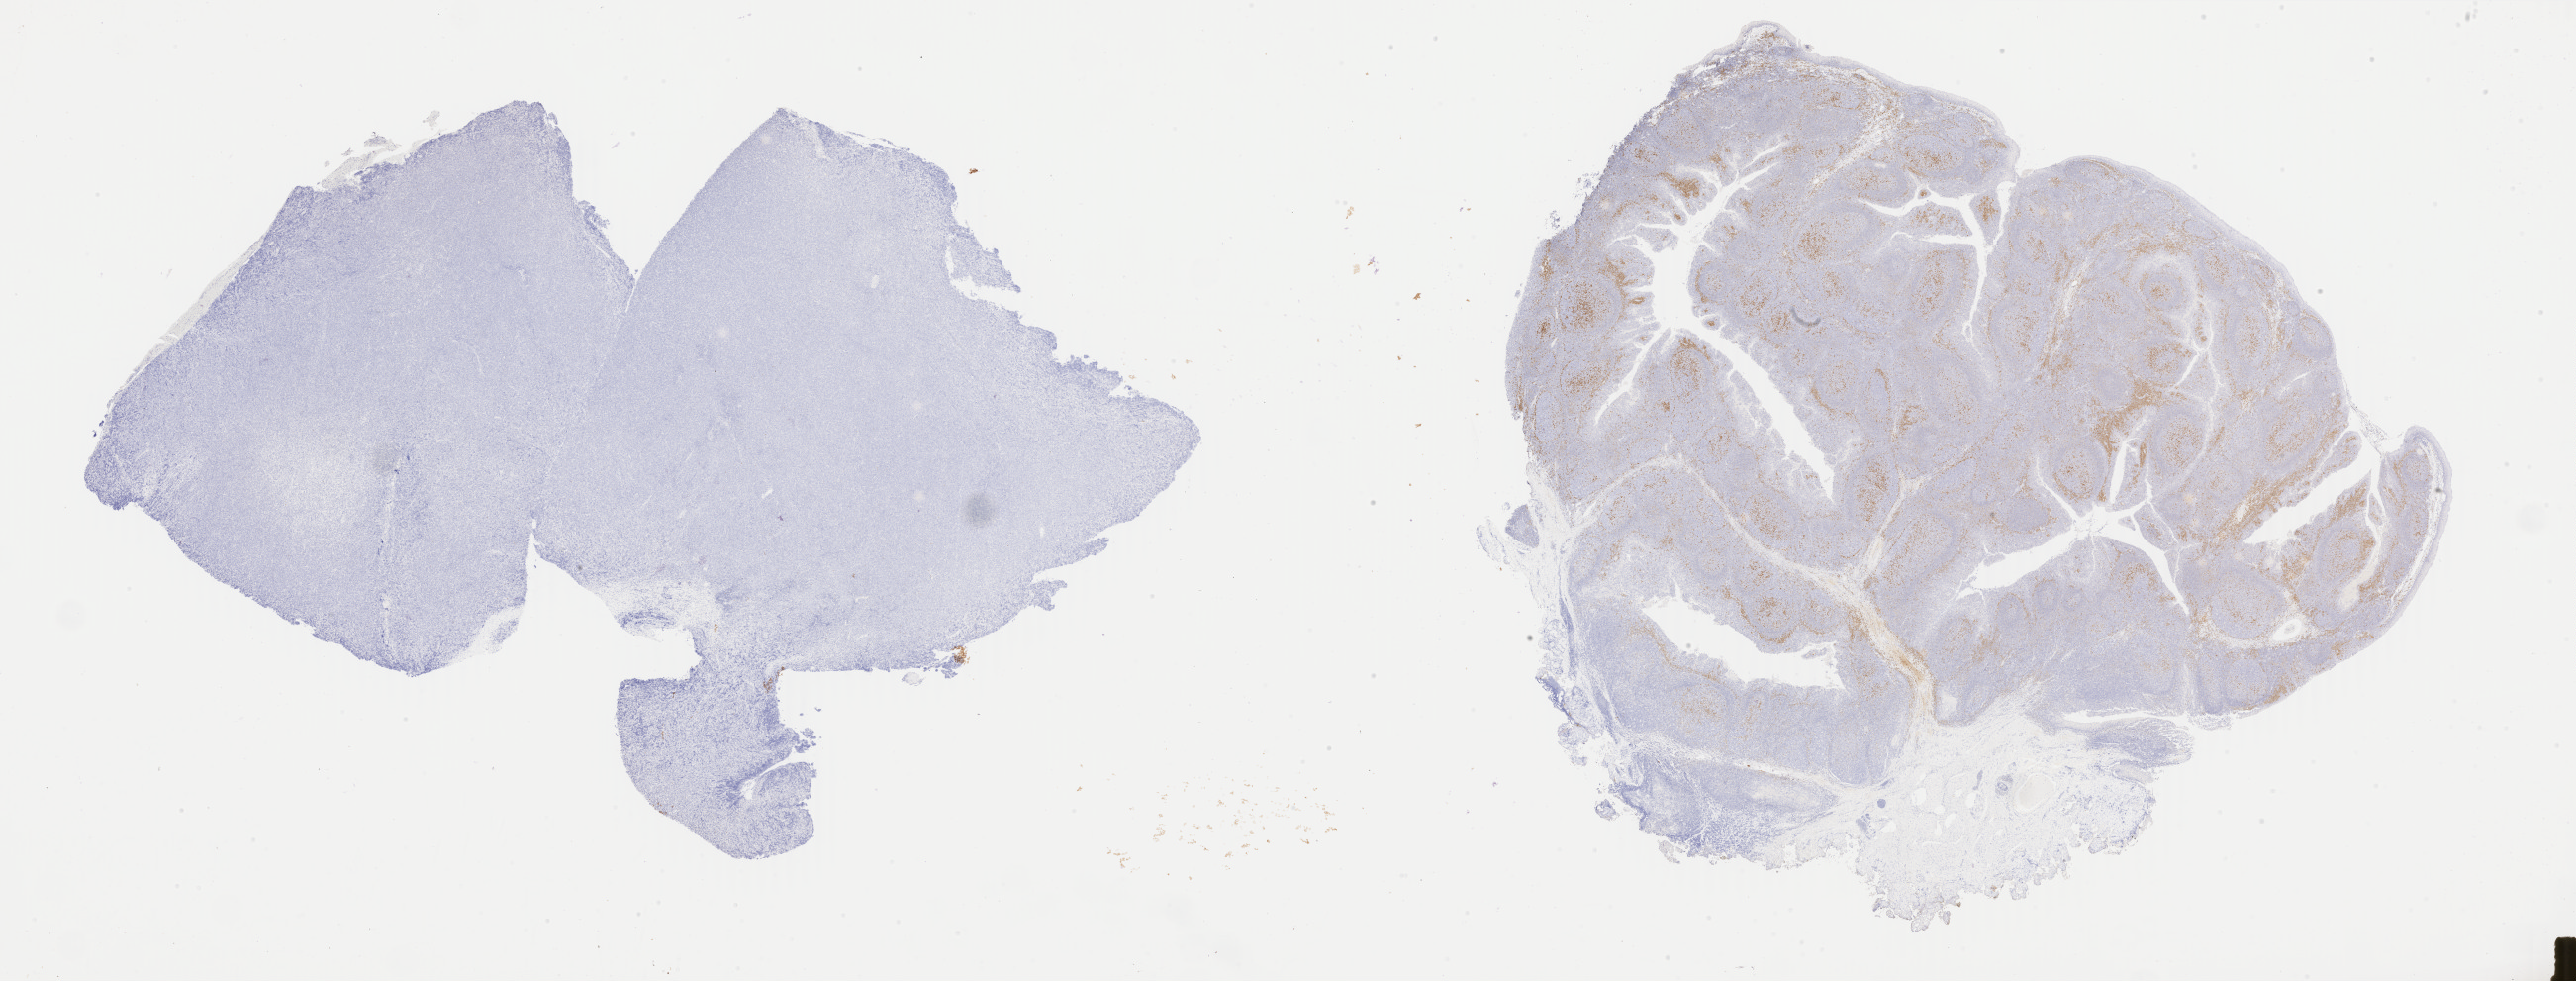
IHC for IRF4/MUM1, whole-slide image — a low-resolution overview of the entire scanned area, about 41.4 x 15.8 mm, tumor tissue. Male, age 7 years at initial diagnosis.
* histologic diagnosis: Diffuse large B-cell lymphoma, NOS